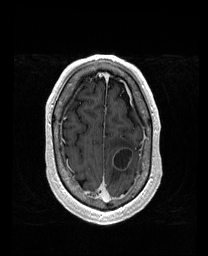
Brain MRI from a brain-tumour surgery series, one axial slice; position 146 of 192 along the scan axis; T1-weighted post-contrast; 208 × 256 image matrix, field of view 211 × 260 mm. Case-level facts recorded for this patient, not image findings: histopathology: Metastatic Carcinoma from Lung Adenocarcinoma; tumour location: Left Frontal.
Structures marked on this image (outlined manually by an expert reader):
- tumour: box from (x=113, y=148) to (x=133, y=171) px